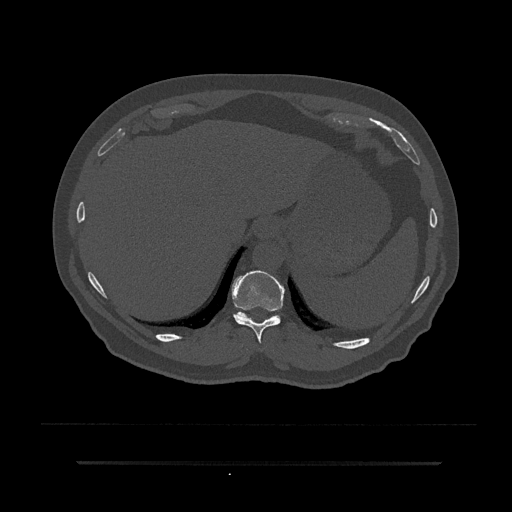
CT including the spine, one axial slice; position 314 of 797 along the scan axis; bone window (W 1800 / L 400 HU); 0.5 mm slice thickness; 512 × 512 image matrix. Patient: male, 59 years. From the clinical record (not read from this slice): primary cancer: bile ducts; vertebrae with lytic lesions (as recorded): T10.
Annotated regions visible in this slice (semi-automatically segmented with operator editing):
- T10 vertebra: box from (x=232, y=271) to (x=285, y=343) px
- T11 vertebra: (x=235, y=312)–(x=280, y=320)